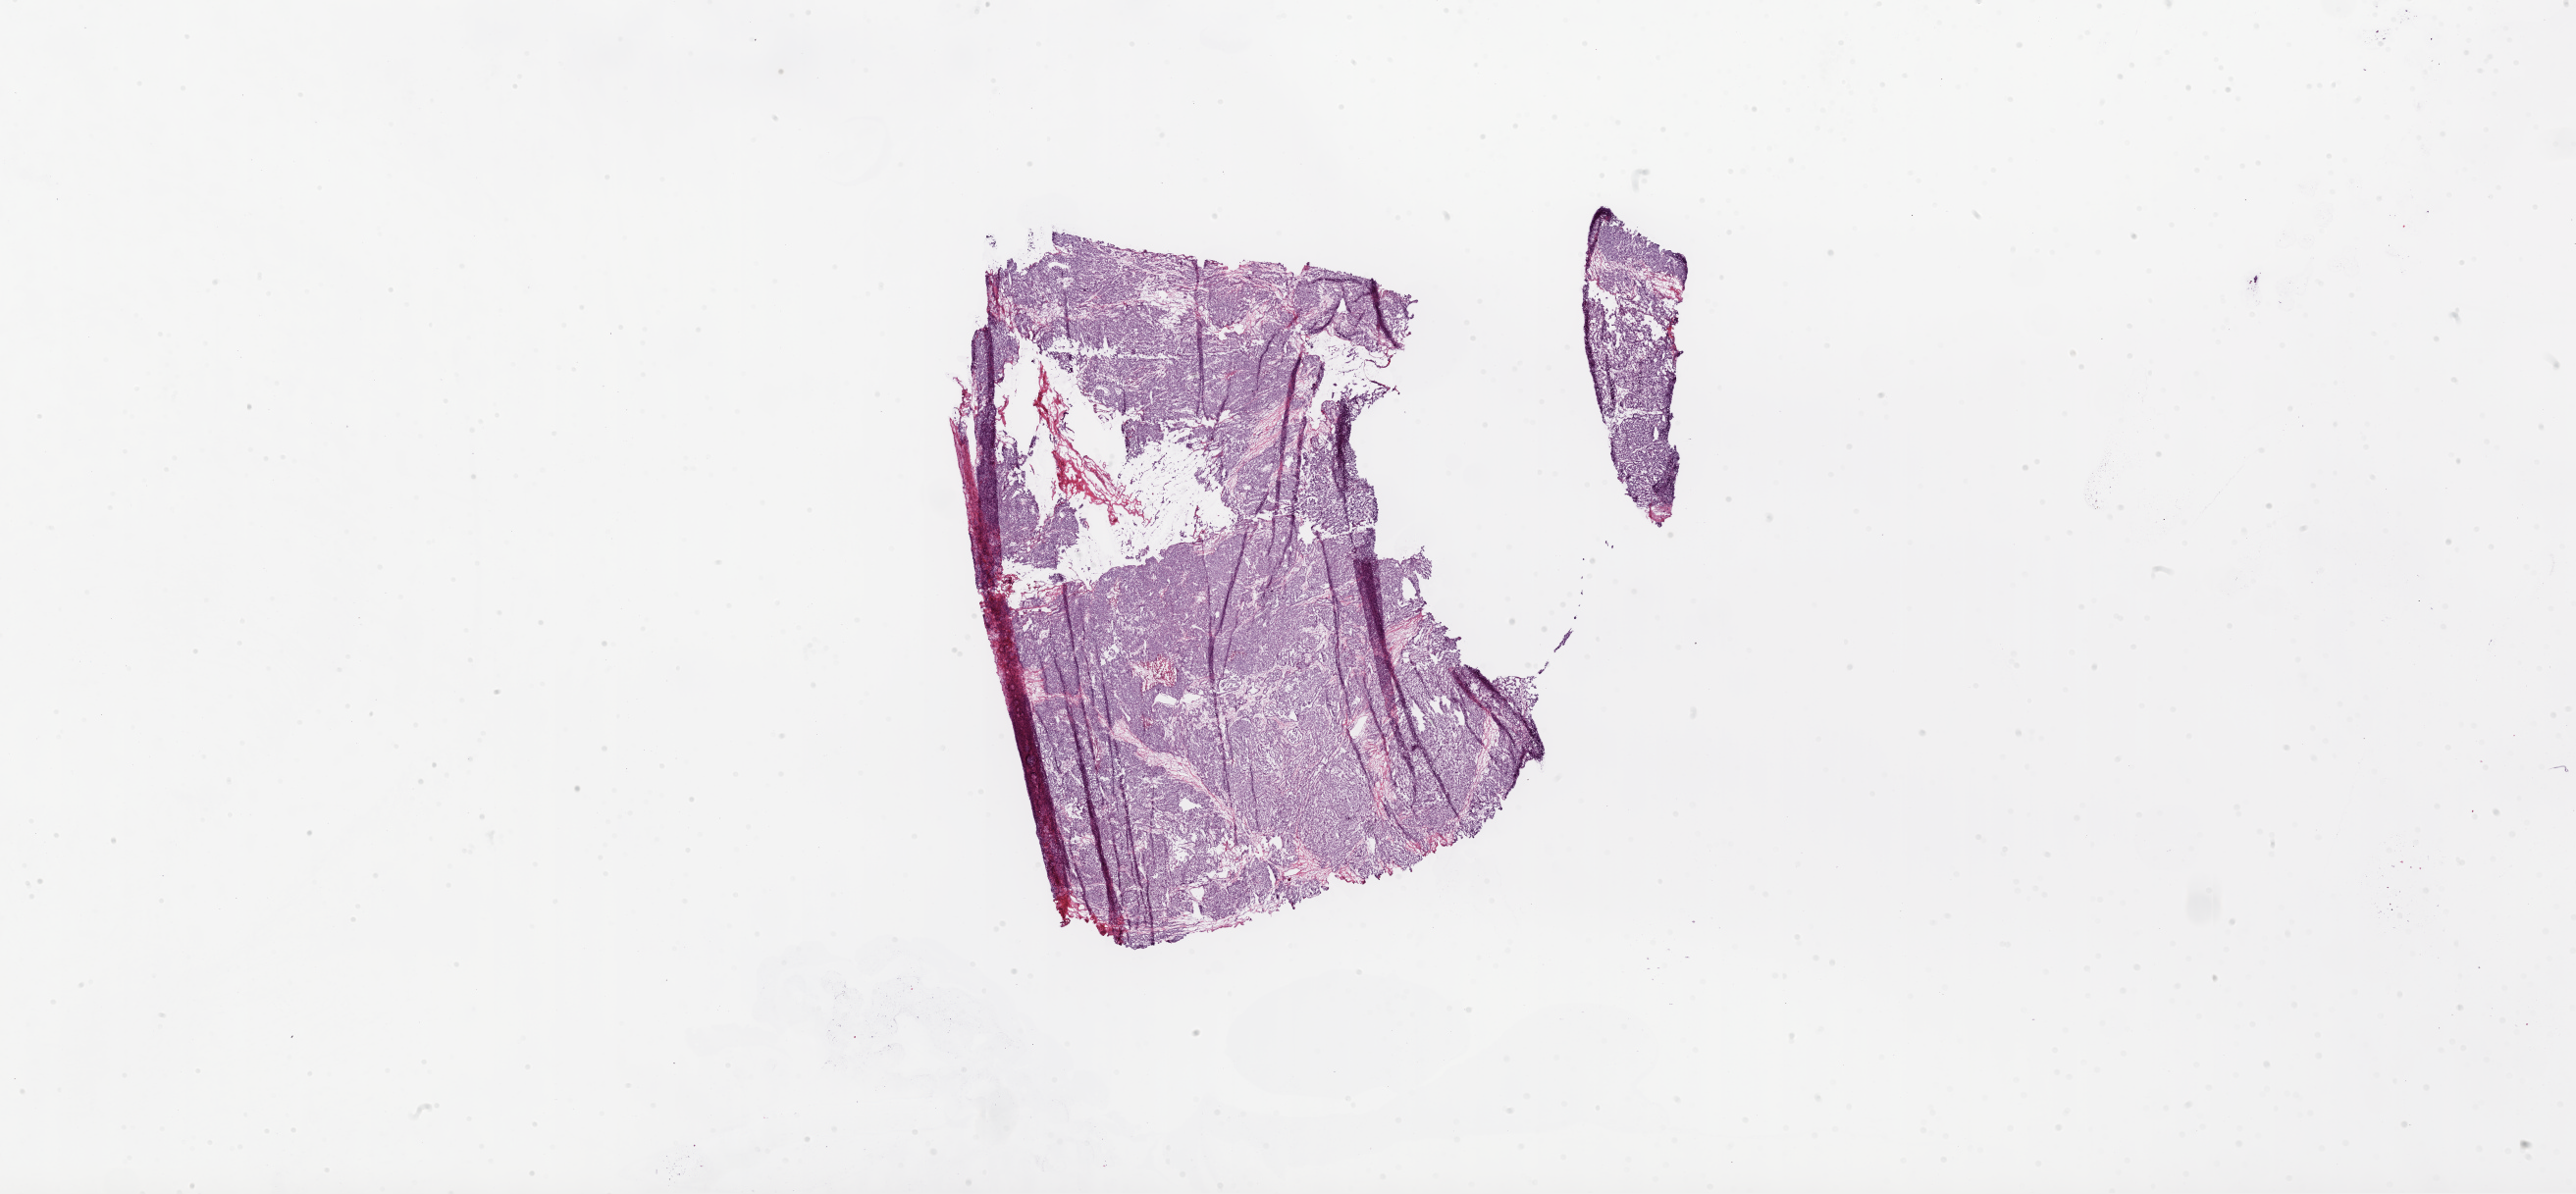
Whole-slide histology image, Hematoxylin and eosin (H&E) stained, whole scanned area (about 42.1 x 19.5 mm, acquisition: 20x scan) shown as a low-resolution overview; frozen section from the top of the tissue portion; primary tumour sample from the ovary. Female patient; age at initial diagnosis 58 years. Histologic grade: G3 (poorly differentiated). Slide review estimates, as recorded: tumour cells 95%, tumour nuclei 95%, normal cells 0%, stromal cells 4%, necrosis 1%.
Diagnosis: Serous cystadenocarcinoma, NOS. FIGO stage: IIB.